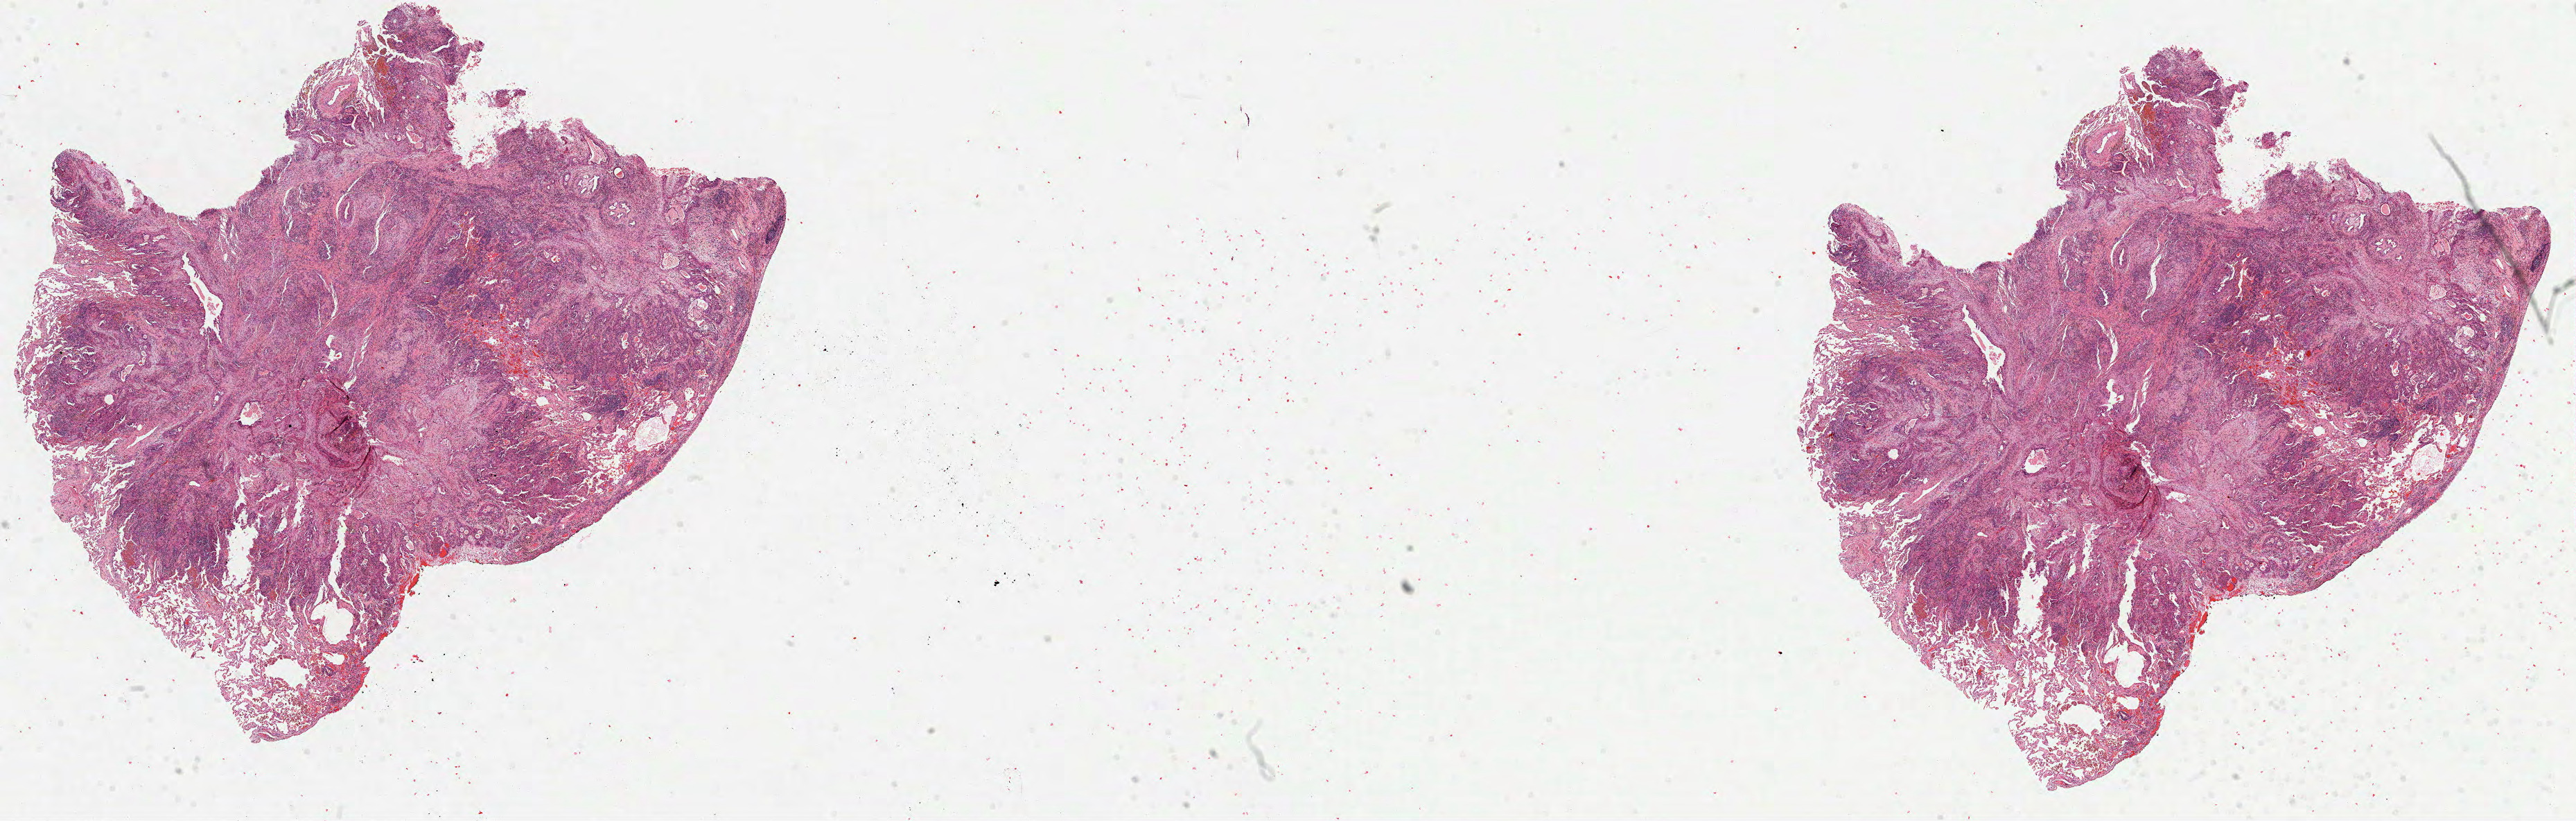
Whole-slide histology image, Hematoxylin and eosin (H&E) stained, whole scanned area (about 30.0 x 9.5 mm) shown as a low-resolution overview, formalin-fixed paraffin-embedded (FFPE) diagnostic section, sample: primary tumour, lung. Patient: female, age at initial diagnosis 62 years.
Histologic diagnosis: Squamous cell carcinoma, NOS (lower lobe, lung). AJCC pathologic stage: IA.